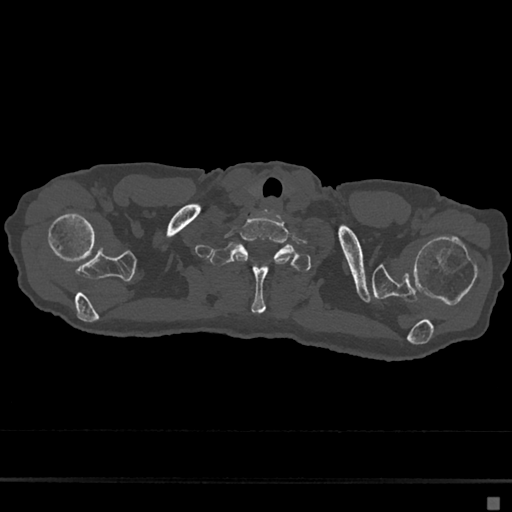
CT including the spine, one axial slice. Slice 625 of 797 in the series (ordered by position). Reconstruction kernel Br40s/3. 120 kVp. Bone window (W 1800 / L 400 HU). 512 × 512 image matrix, field of view 360 × 360 mm. Patient: female, 68 years. Case-level facts recorded for this patient, not image findings: primary cancer: renal.
Annotated regions visible in this slice (semi-automatic segmentation, software-assisted and operator-edited):
- T1 vertebra: box from (x=209, y=243) to (x=312, y=314) px